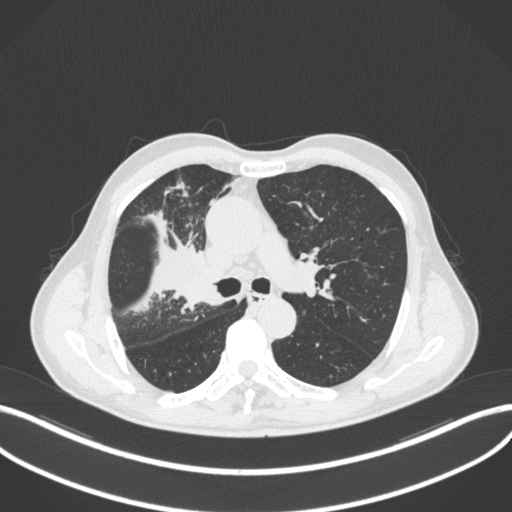
Chest CT, one axial slice; slice 314 of 490 in the series (ordered by position); reconstruction kernel B31f; 120 kVp; lung window (W 1500 / L -600 HU); 512 × 512 image matrix. Patient: male, 69 years. From the clinical record (not read from this slice): clinical TNM (as recorded): T2a N0 M0.
Outlined on this slice (bounding box drawn by a radiologist):
- lung tumour (recorded histology: adenocarcinoma): bounding box [x1, y1, x2, y2] px = [165, 259, 216, 311]